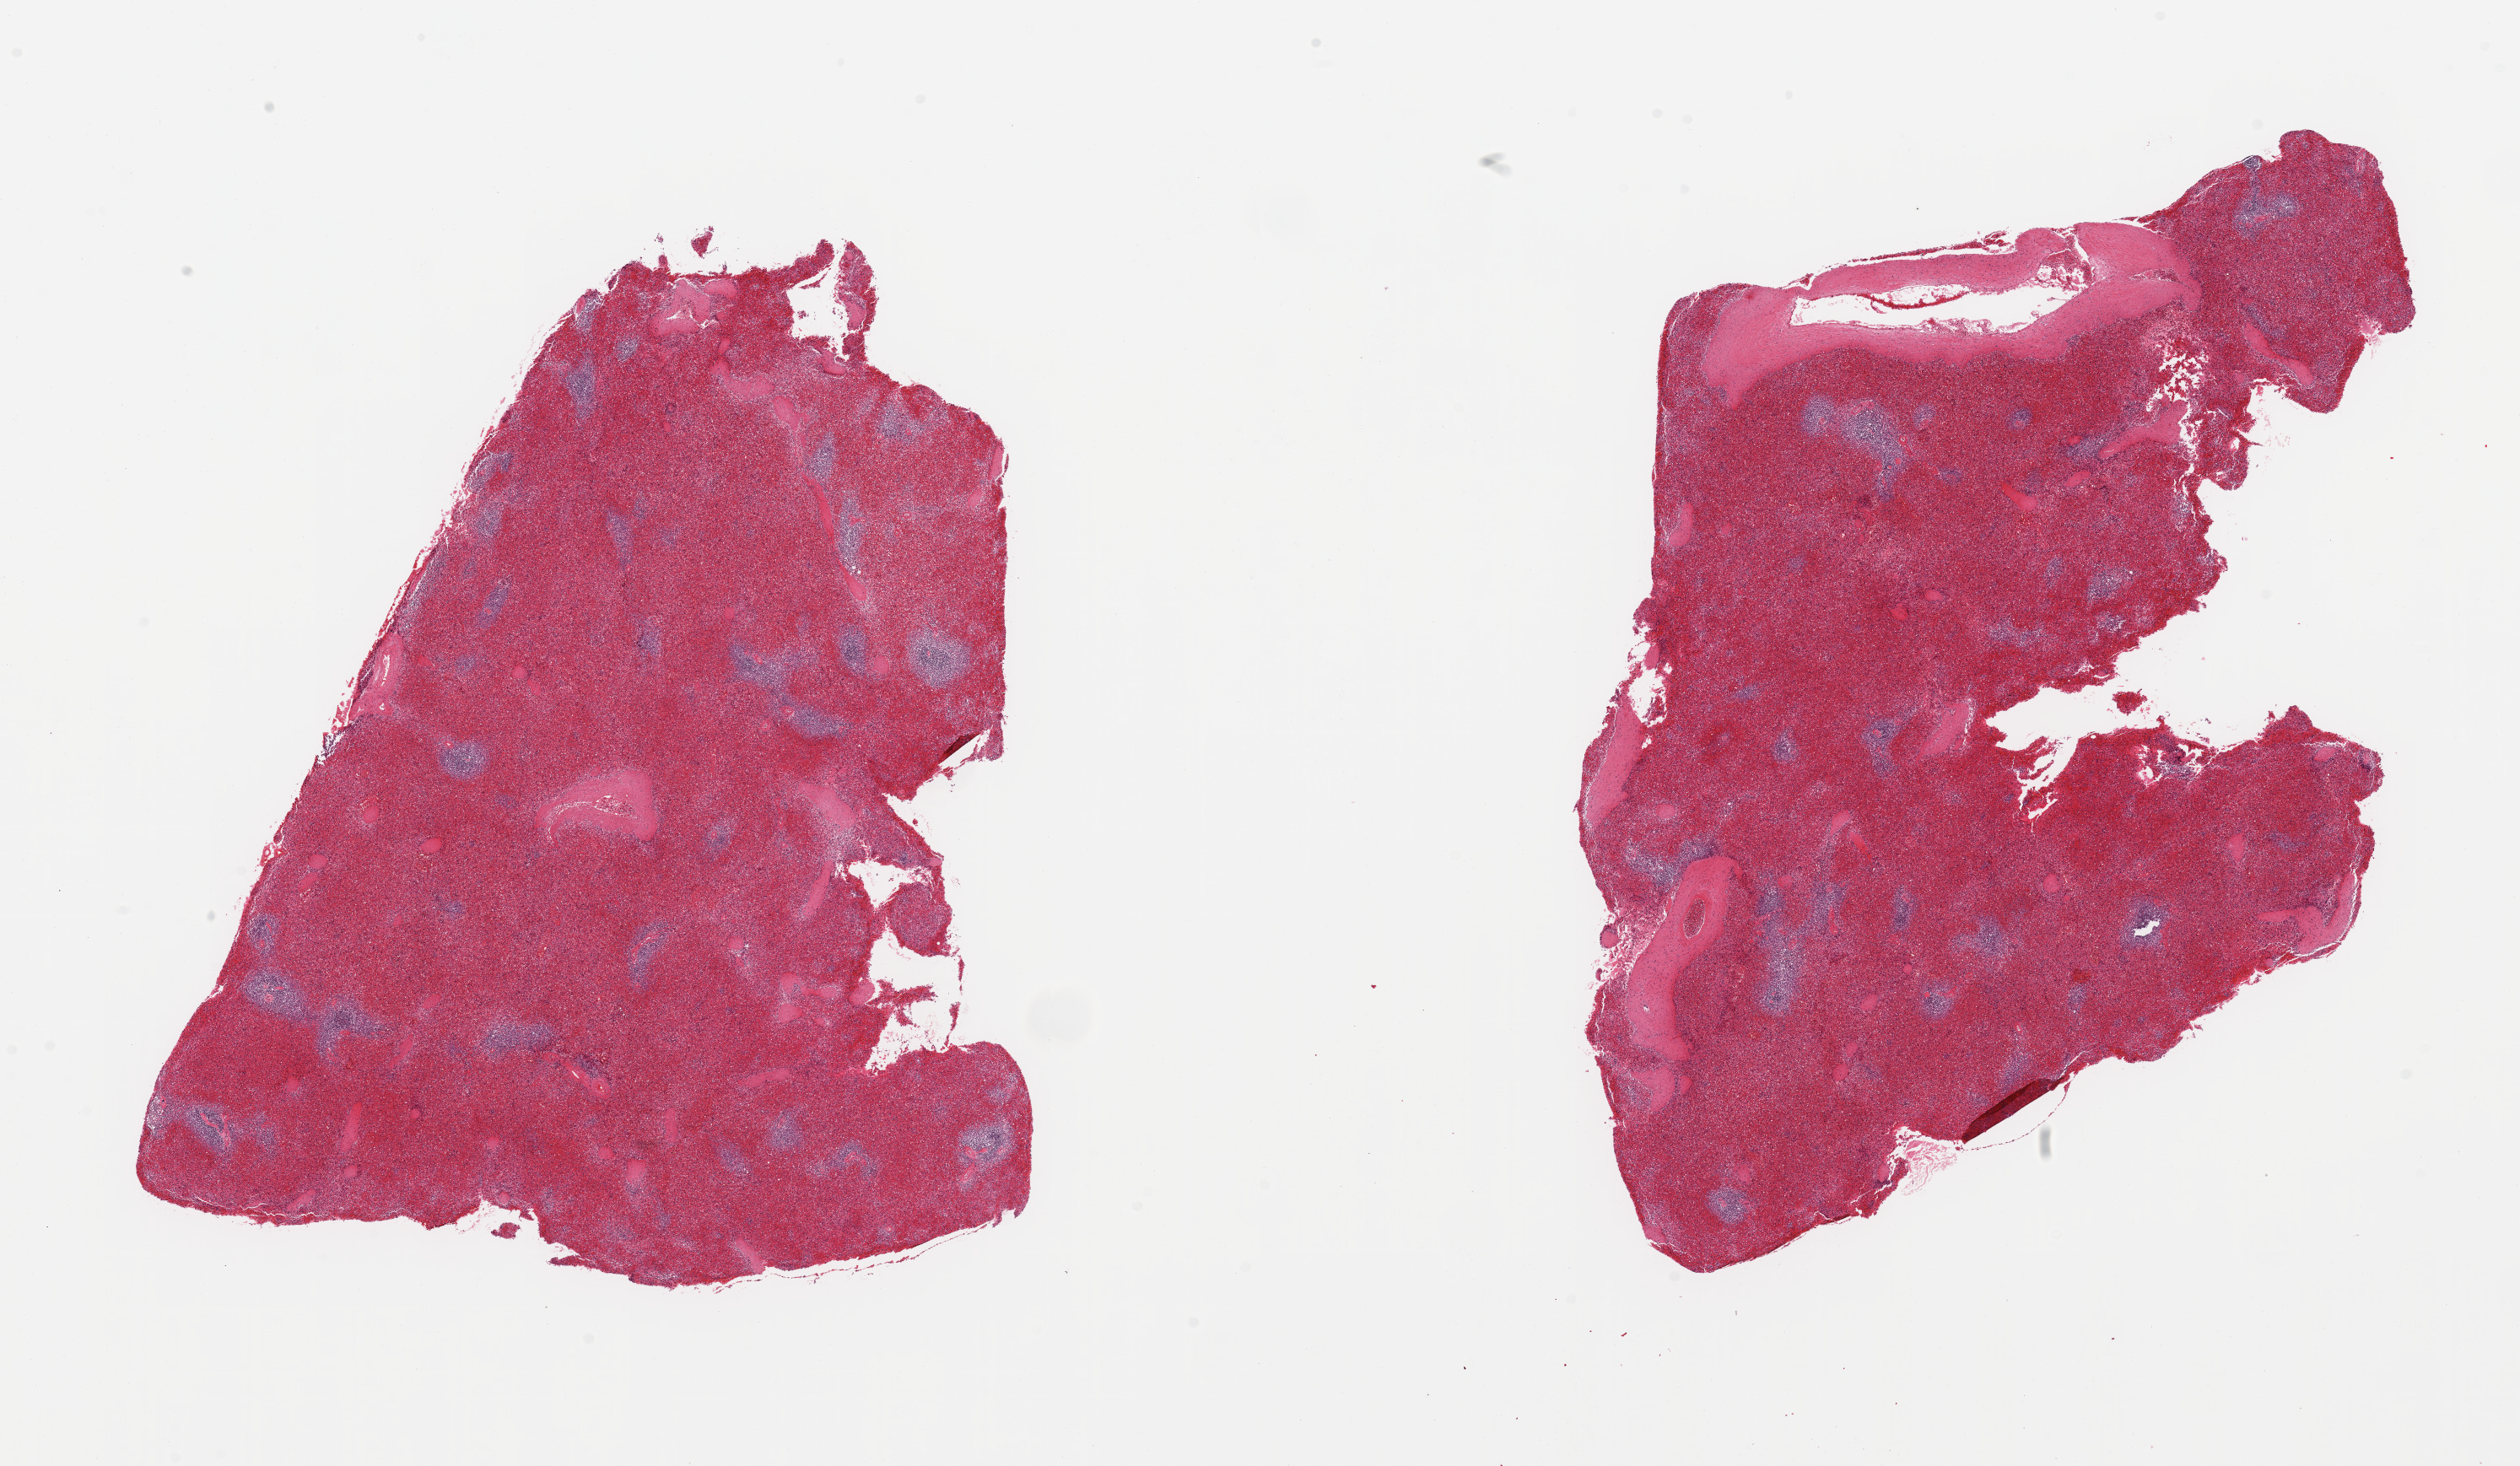
Whole-slide image, hematoxylin and eosin (H&E) stain — whole scanned area (about 23.6 x 13.7 mm) shown as a low-resolution overview; PAXgene-fixed, paraffin-embedded tissue; section of spleen (target tissue); tissue donor sample. Donor sex: male.
Review note (as recorded): 2 pieces, no abnormalities.